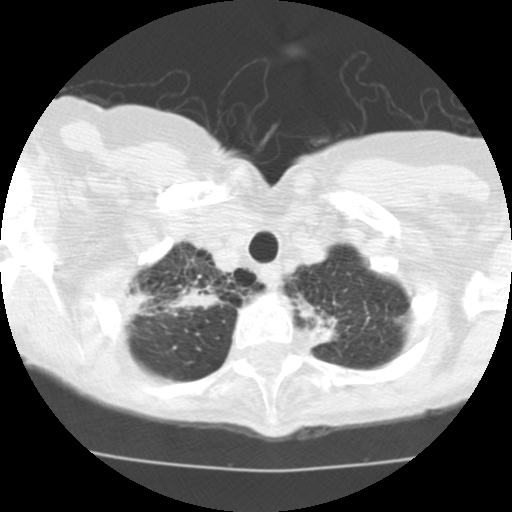
Low-dose screening chest CT, one axial slice. Position 105 of 115 along the scan axis. Reconstruction kernel STANDARD. 120 kVp. Lung window (W 1500 / L -600 HU). 512 × 512 image matrix.
Outlined on this slice (manually delineated by an expert):
- lesion 1 (tumor, upper lobe of right lung): bounding box <126,287,154,321> (left, top, right, bottom; pixels)